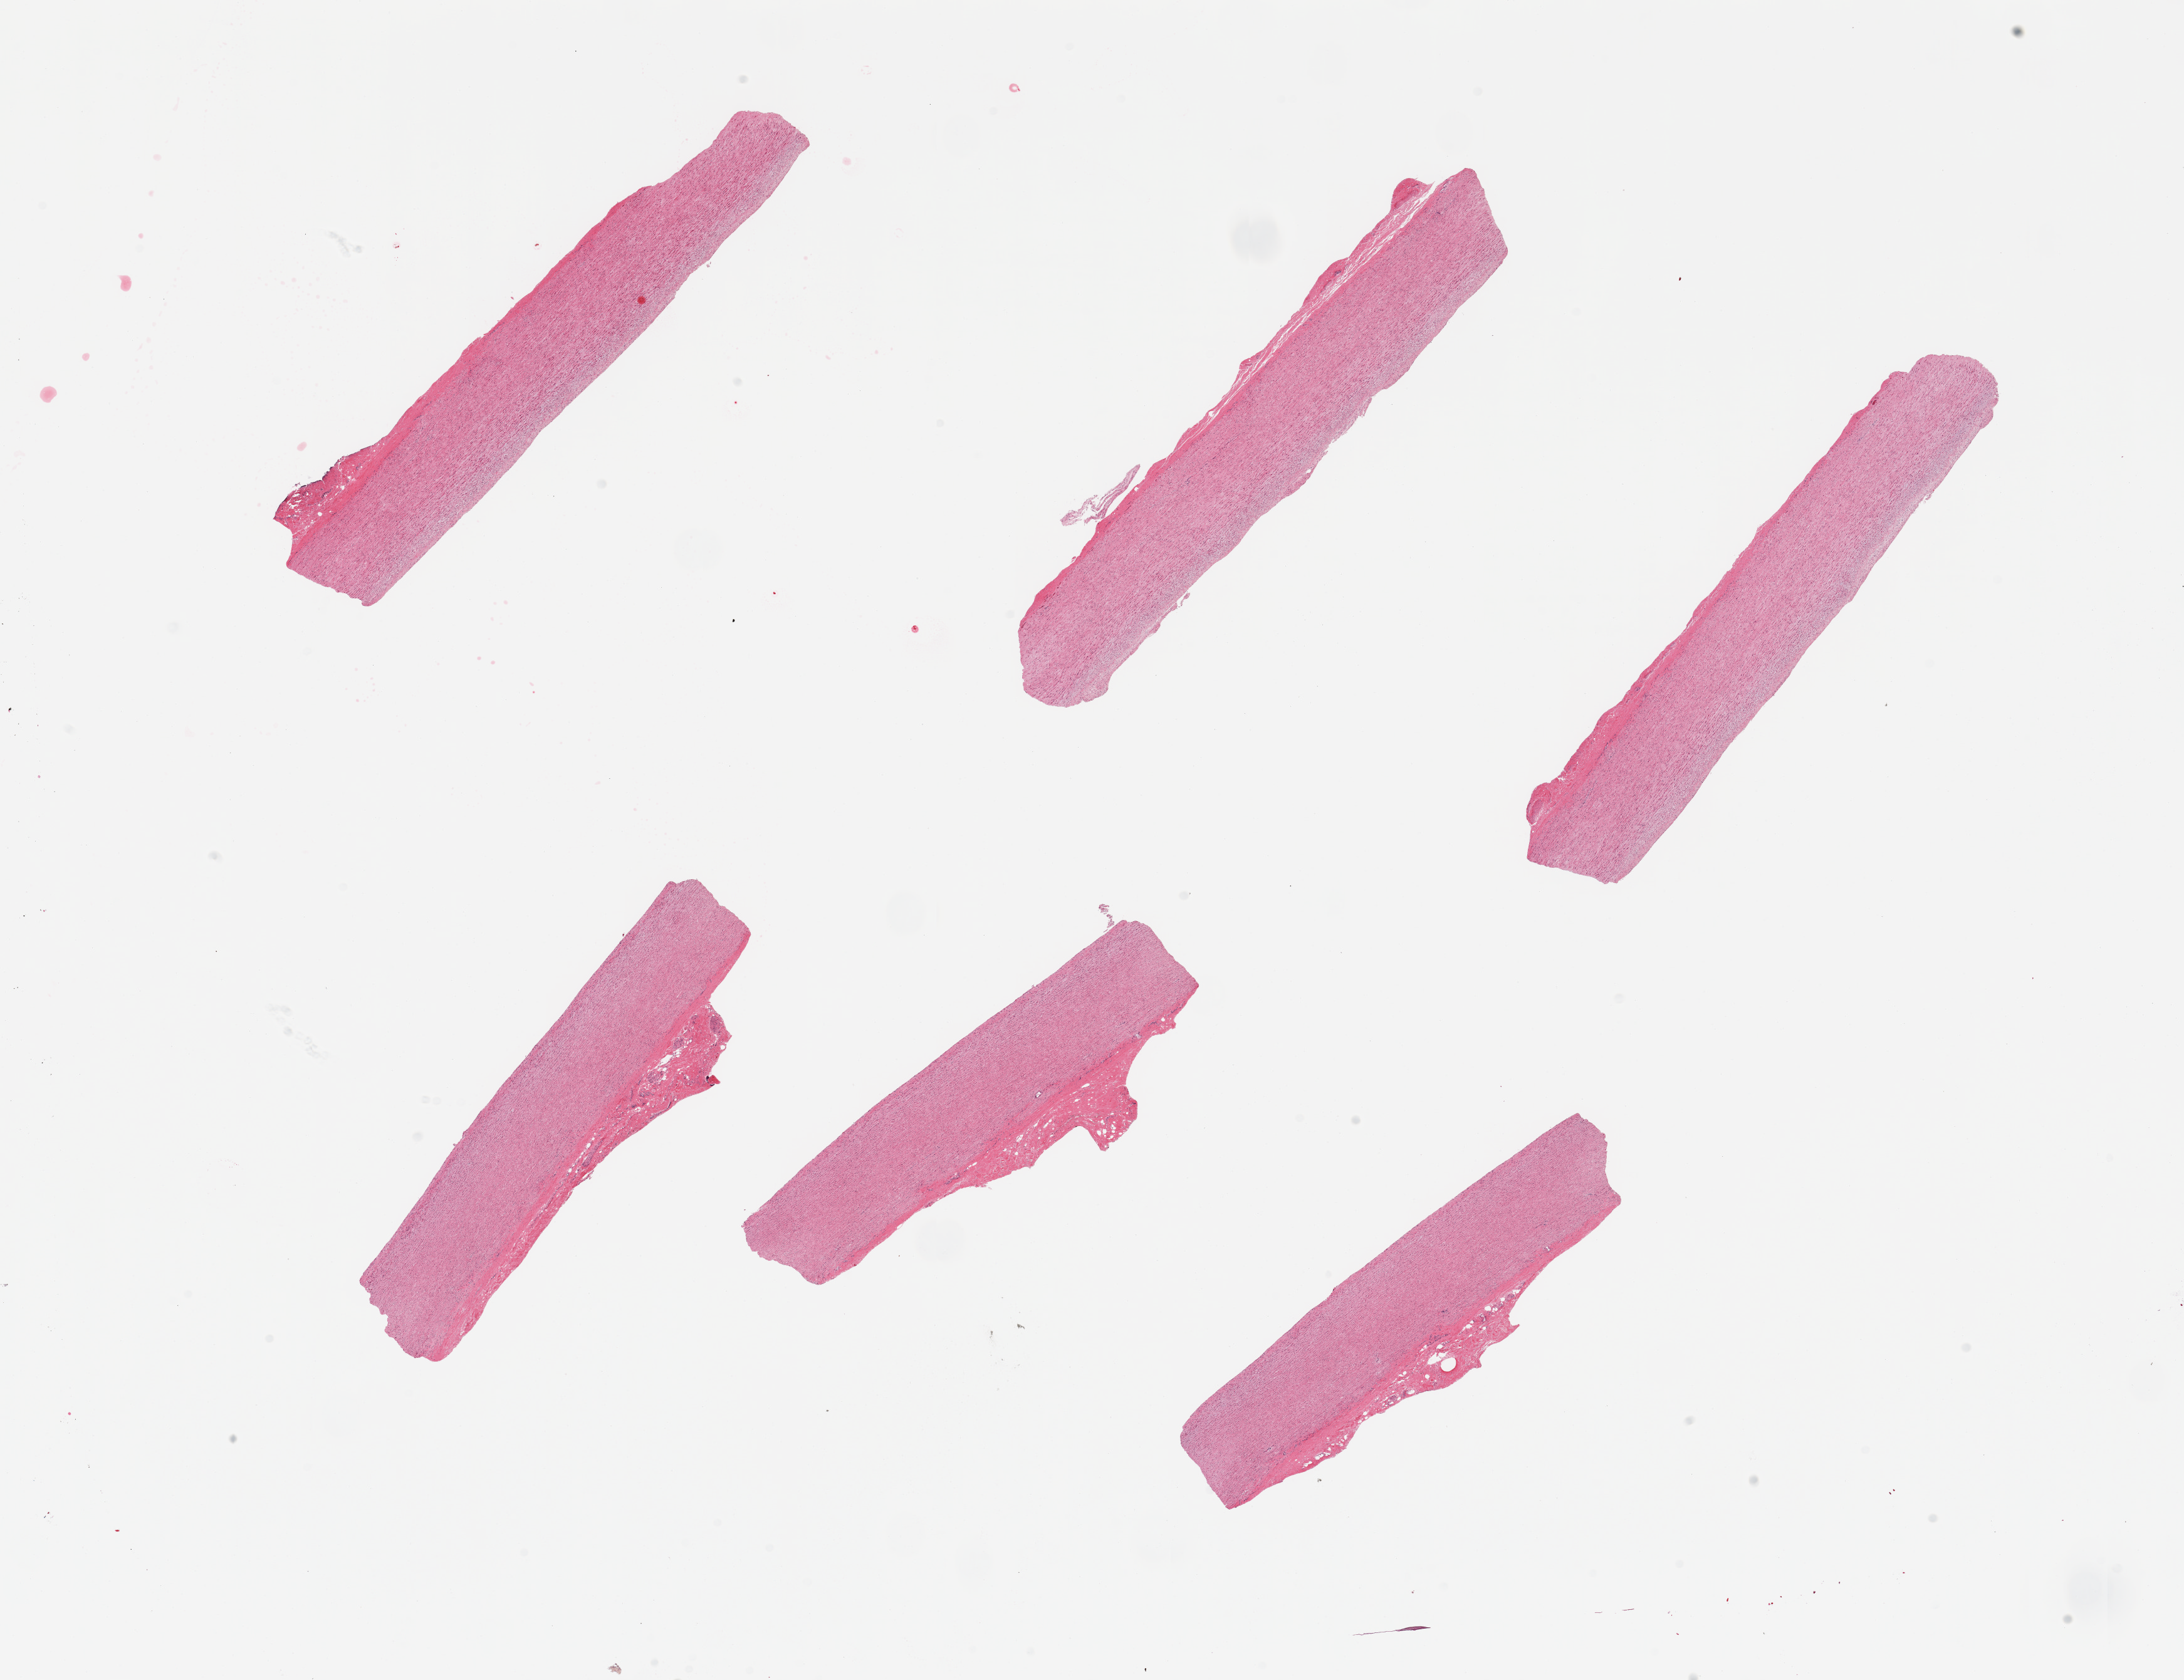
Hematoxylin and eosin (H&E) whole-slide image — whole scanned area (about 27.6 x 21.2 mm, acquisition: 20x scan) shown as a low-resolution overview, PAXgene-fixed, paraffin-embedded tissue, target tissue: aorta, donor tissue sample. Donor sex: male.
Pathologist's review note for this sample: 6 pieces; some attached adventitia/nerve.